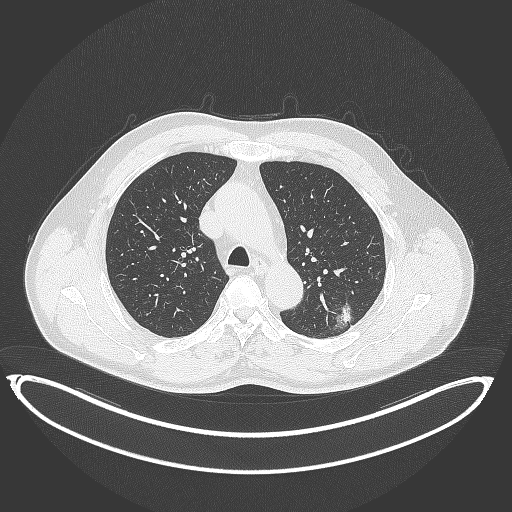
Chest CT, one axial slice; position 255 of 399 along the scan axis; reconstruction kernel B70f; lung window (W 1500 / L -600 HU); 1 mm slice thickness; 512 × 512 image matrix. Male patient, age 58 years. Case-level facts recorded for this patient, not image findings: clinical TNM (as recorded): T1c N0 M0.
Annotated regions visible in this slice (rectangle marked by the reading radiologist):
- lung tumour (recorded histology: adenocarcinoma): bounding box <330,295,357,332> (left, top, right, bottom; pixels)